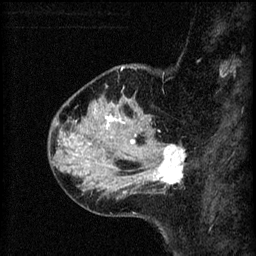
Breast MRI (dynamic contrast-enhanced), one sagittal slice; slice 18 of 60 in the series (ordered by position); 3 images stored at this slice position (order not interpretable as contrast timing); 1.5 T; TE 4.2 ms, TR 8.2 ms; 2 mm slice thickness; 256 × 256 image matrix, field of view 180 × 180 mm. Patient: female, 37 years.
Annotated regions visible in this slice (semi-automatically segmented with operator editing):
- analysis volume of interest (the breast-tissue region the enhancement analysis was run in; not a lesion): box from (x=124, y=138) to (x=186, y=195) px
- tumour enhancement mask (voxels above the 70 % enhancement threshold inside the analysis volume of interest): (x=131, y=140)–(x=185, y=185)